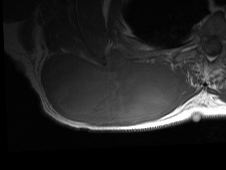
MRI of an extremity soft-tissue mass, one axial slice. MR volume resampled by the dataset authors to the PET/CT grid (not the native acquisition matrix). 3.27 mm slice thickness. 226 × 170 image matrix, field of view 221 × 166 mm. Male patient. Case-level facts recorded for this patient, not image findings: histological type: pleiomorphic spindle cell undifferentiated; grade: high; site of the primary tumour: right parascapusular.
Outlined on this slice (expert contour drawn on MRI and transferred to this co-registered scan by the dataset authors):
- gross tumour volume including surrounding oedema: bounding box [x1, y1, x2, y2] px = [41, 51, 196, 126]
- gross tumour volume (mass): [41, 51, 180, 125]